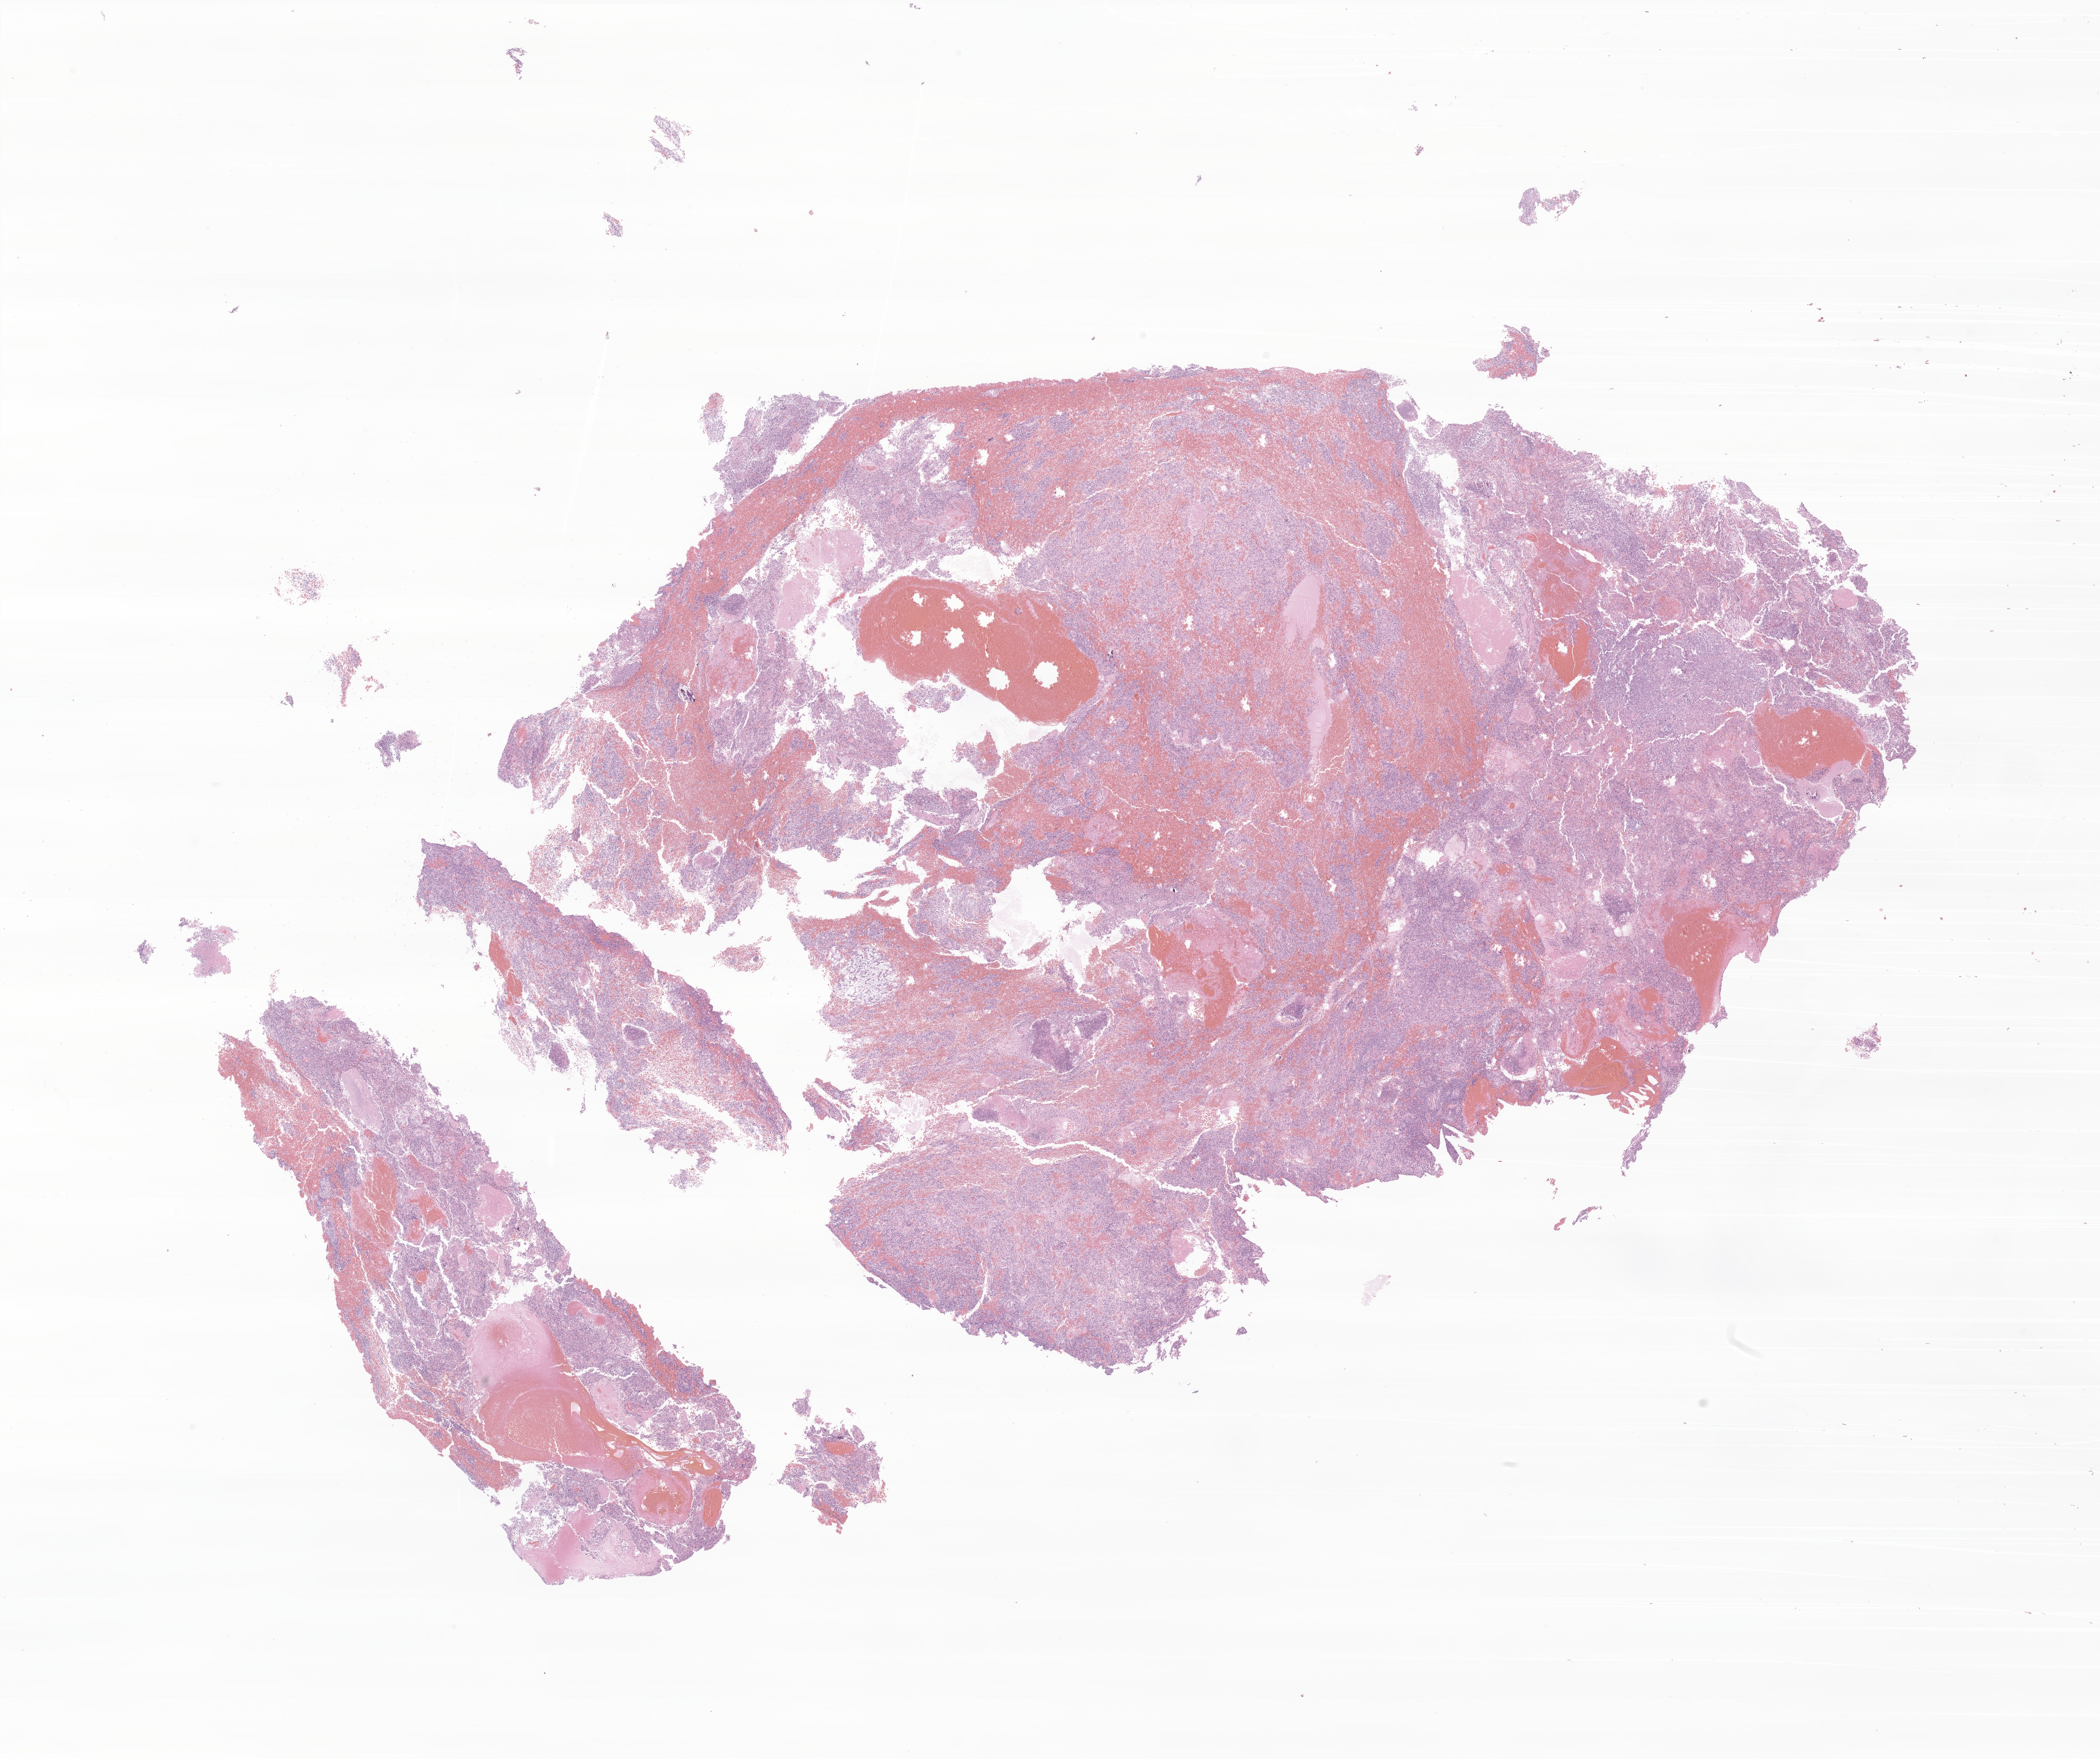
Digitized hematoxylin and eosin (H&E)-stained section of tumor tissue from the brain, whole scanned area (about 22.4 x 18.8 mm) shown as a low-resolution overview, FFPE section. Male patient, age 117 months (9 years 9 months).
Diagnosis (ICD-O-3 morphology term): Neoplasm, uncertain whether benign or malignant.